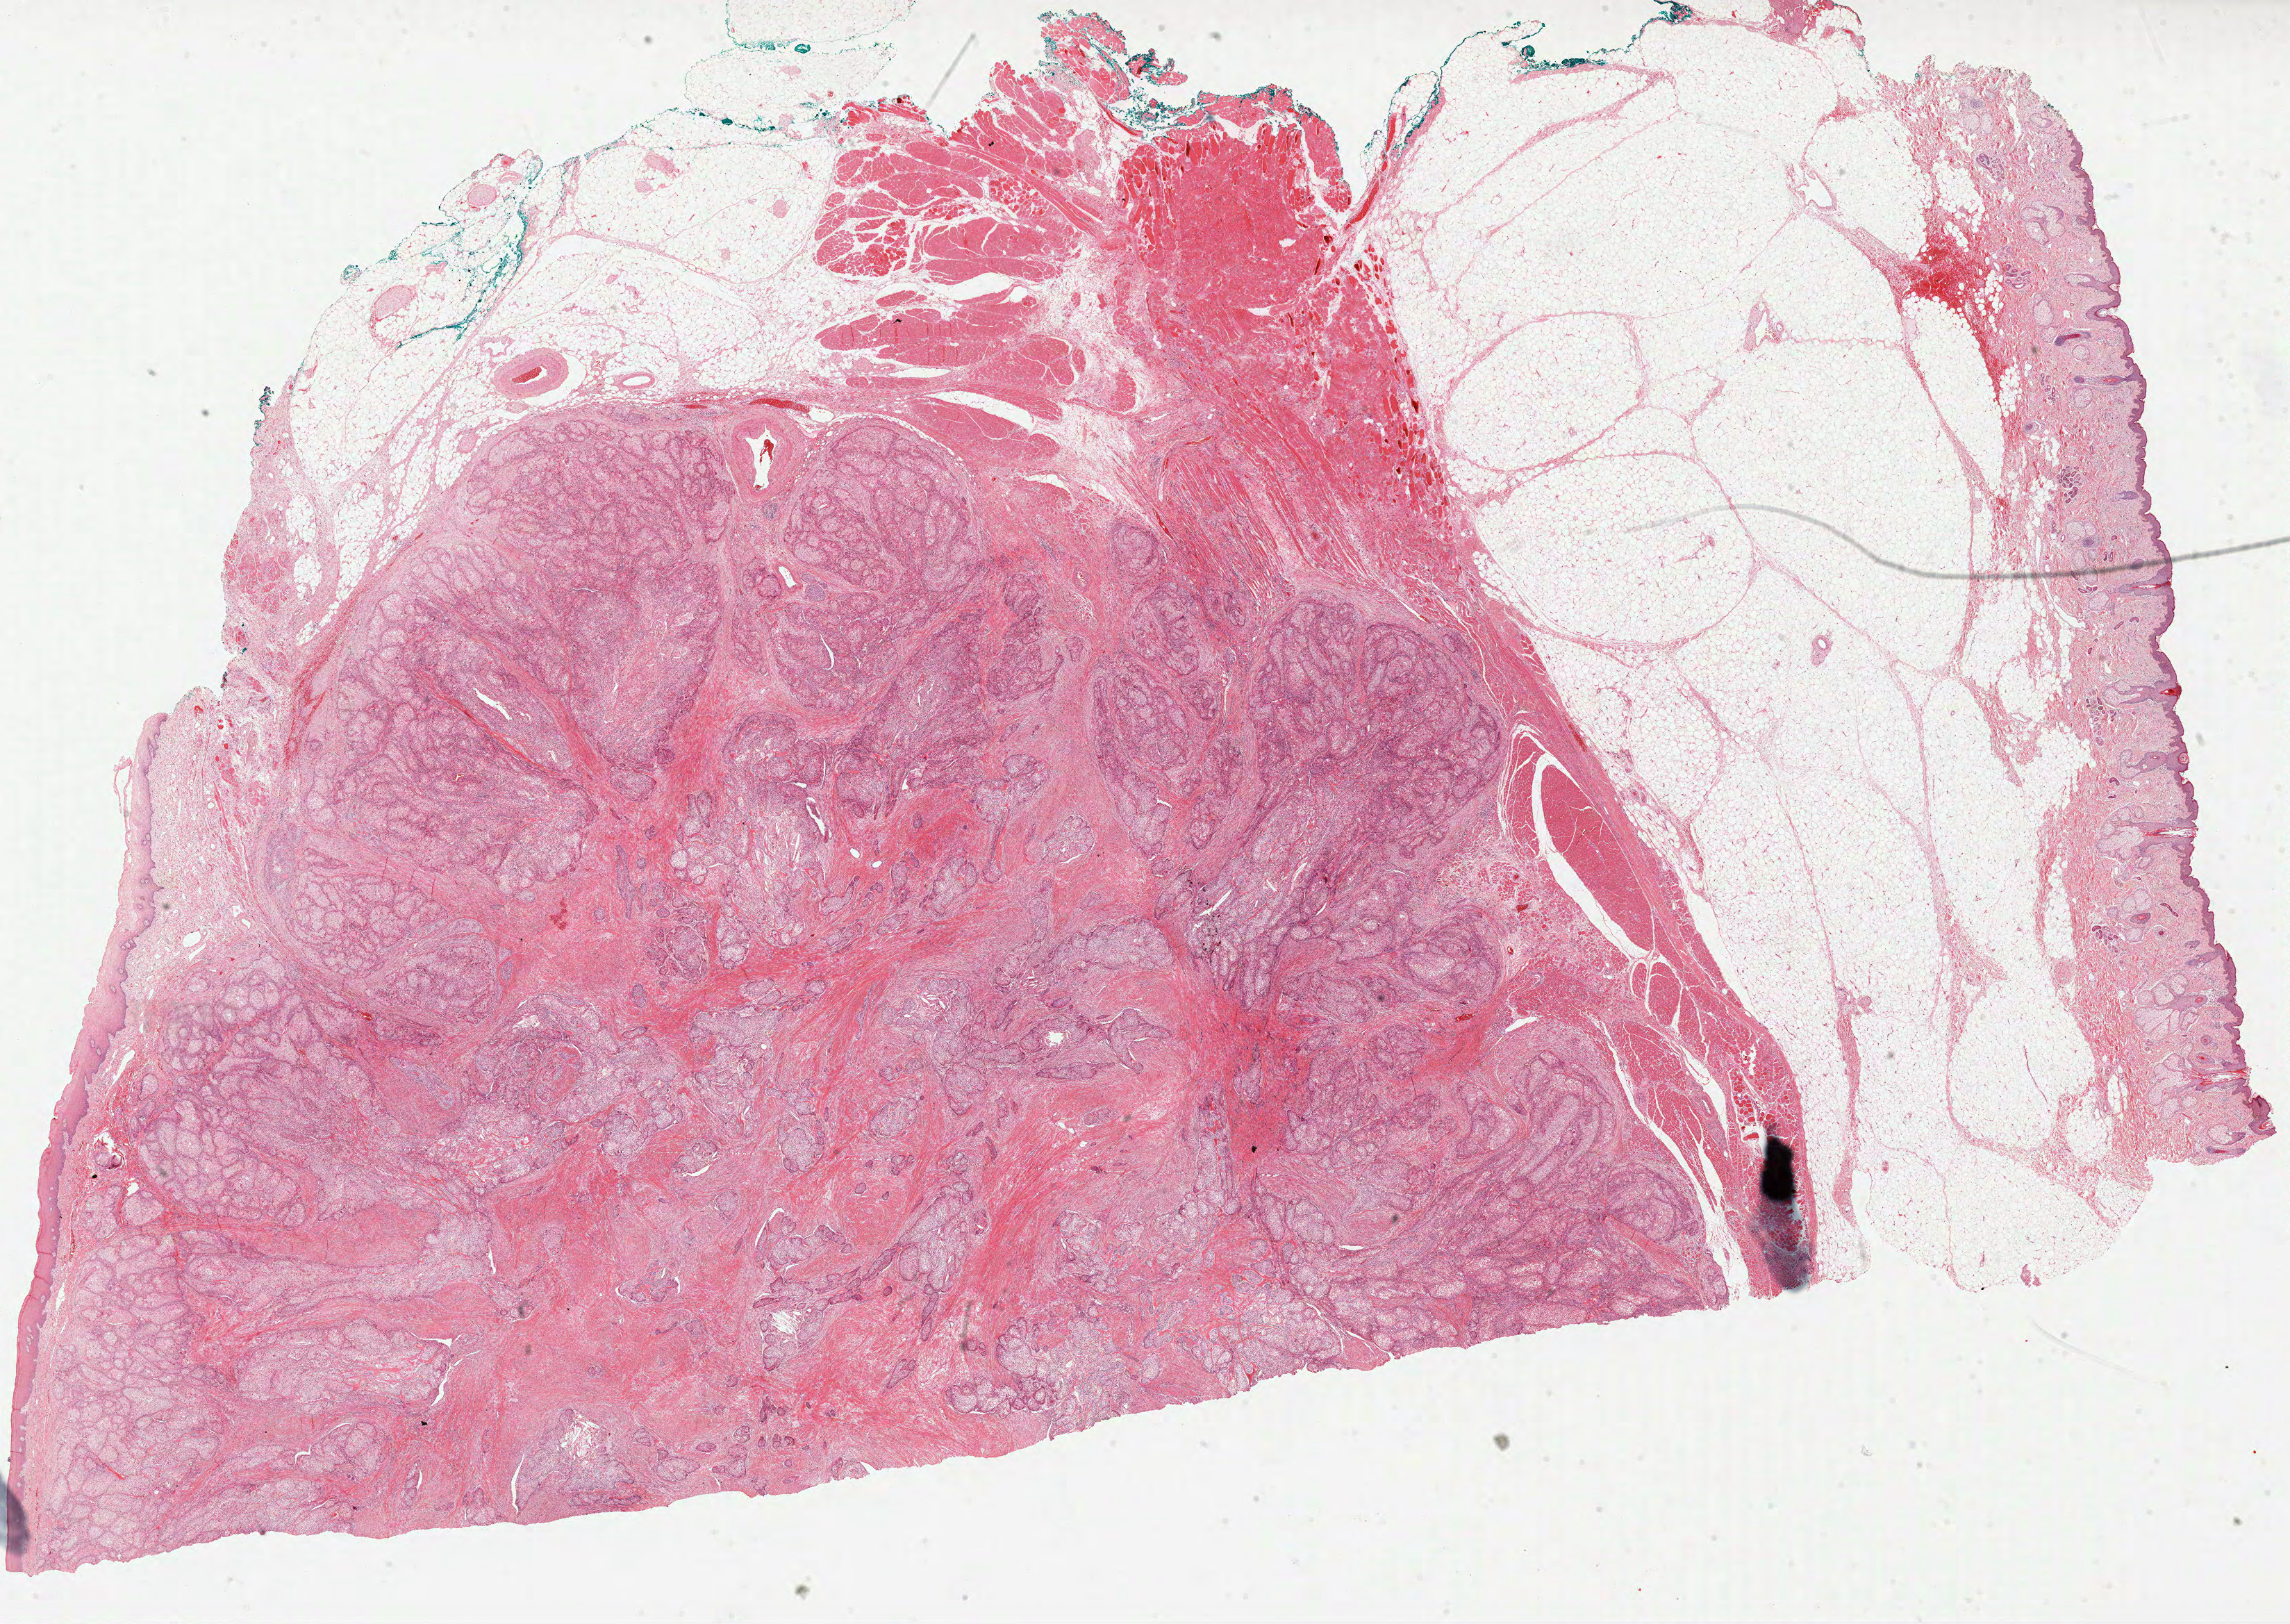
Whole-slide histology image, Hematoxylin and eosin (H&E) stained, whole scanned area (about 26.6 x 18.9 mm, acquisition: 40x scan) shown as a low-resolution overview; formalin-fixed paraffin-embedded (FFPE) diagnostic section; sample: primary tumour, head and neck. Female, age 60 years at initial diagnosis. Histologic grade: G1 (well differentiated).
- histologic diagnosis: Squamous cell carcinoma, NOS (cheek mucosa)
- lymph nodes positive (case pathology): 0 of 48 examined
- laterality: right
- AJCC pathologic stage: II